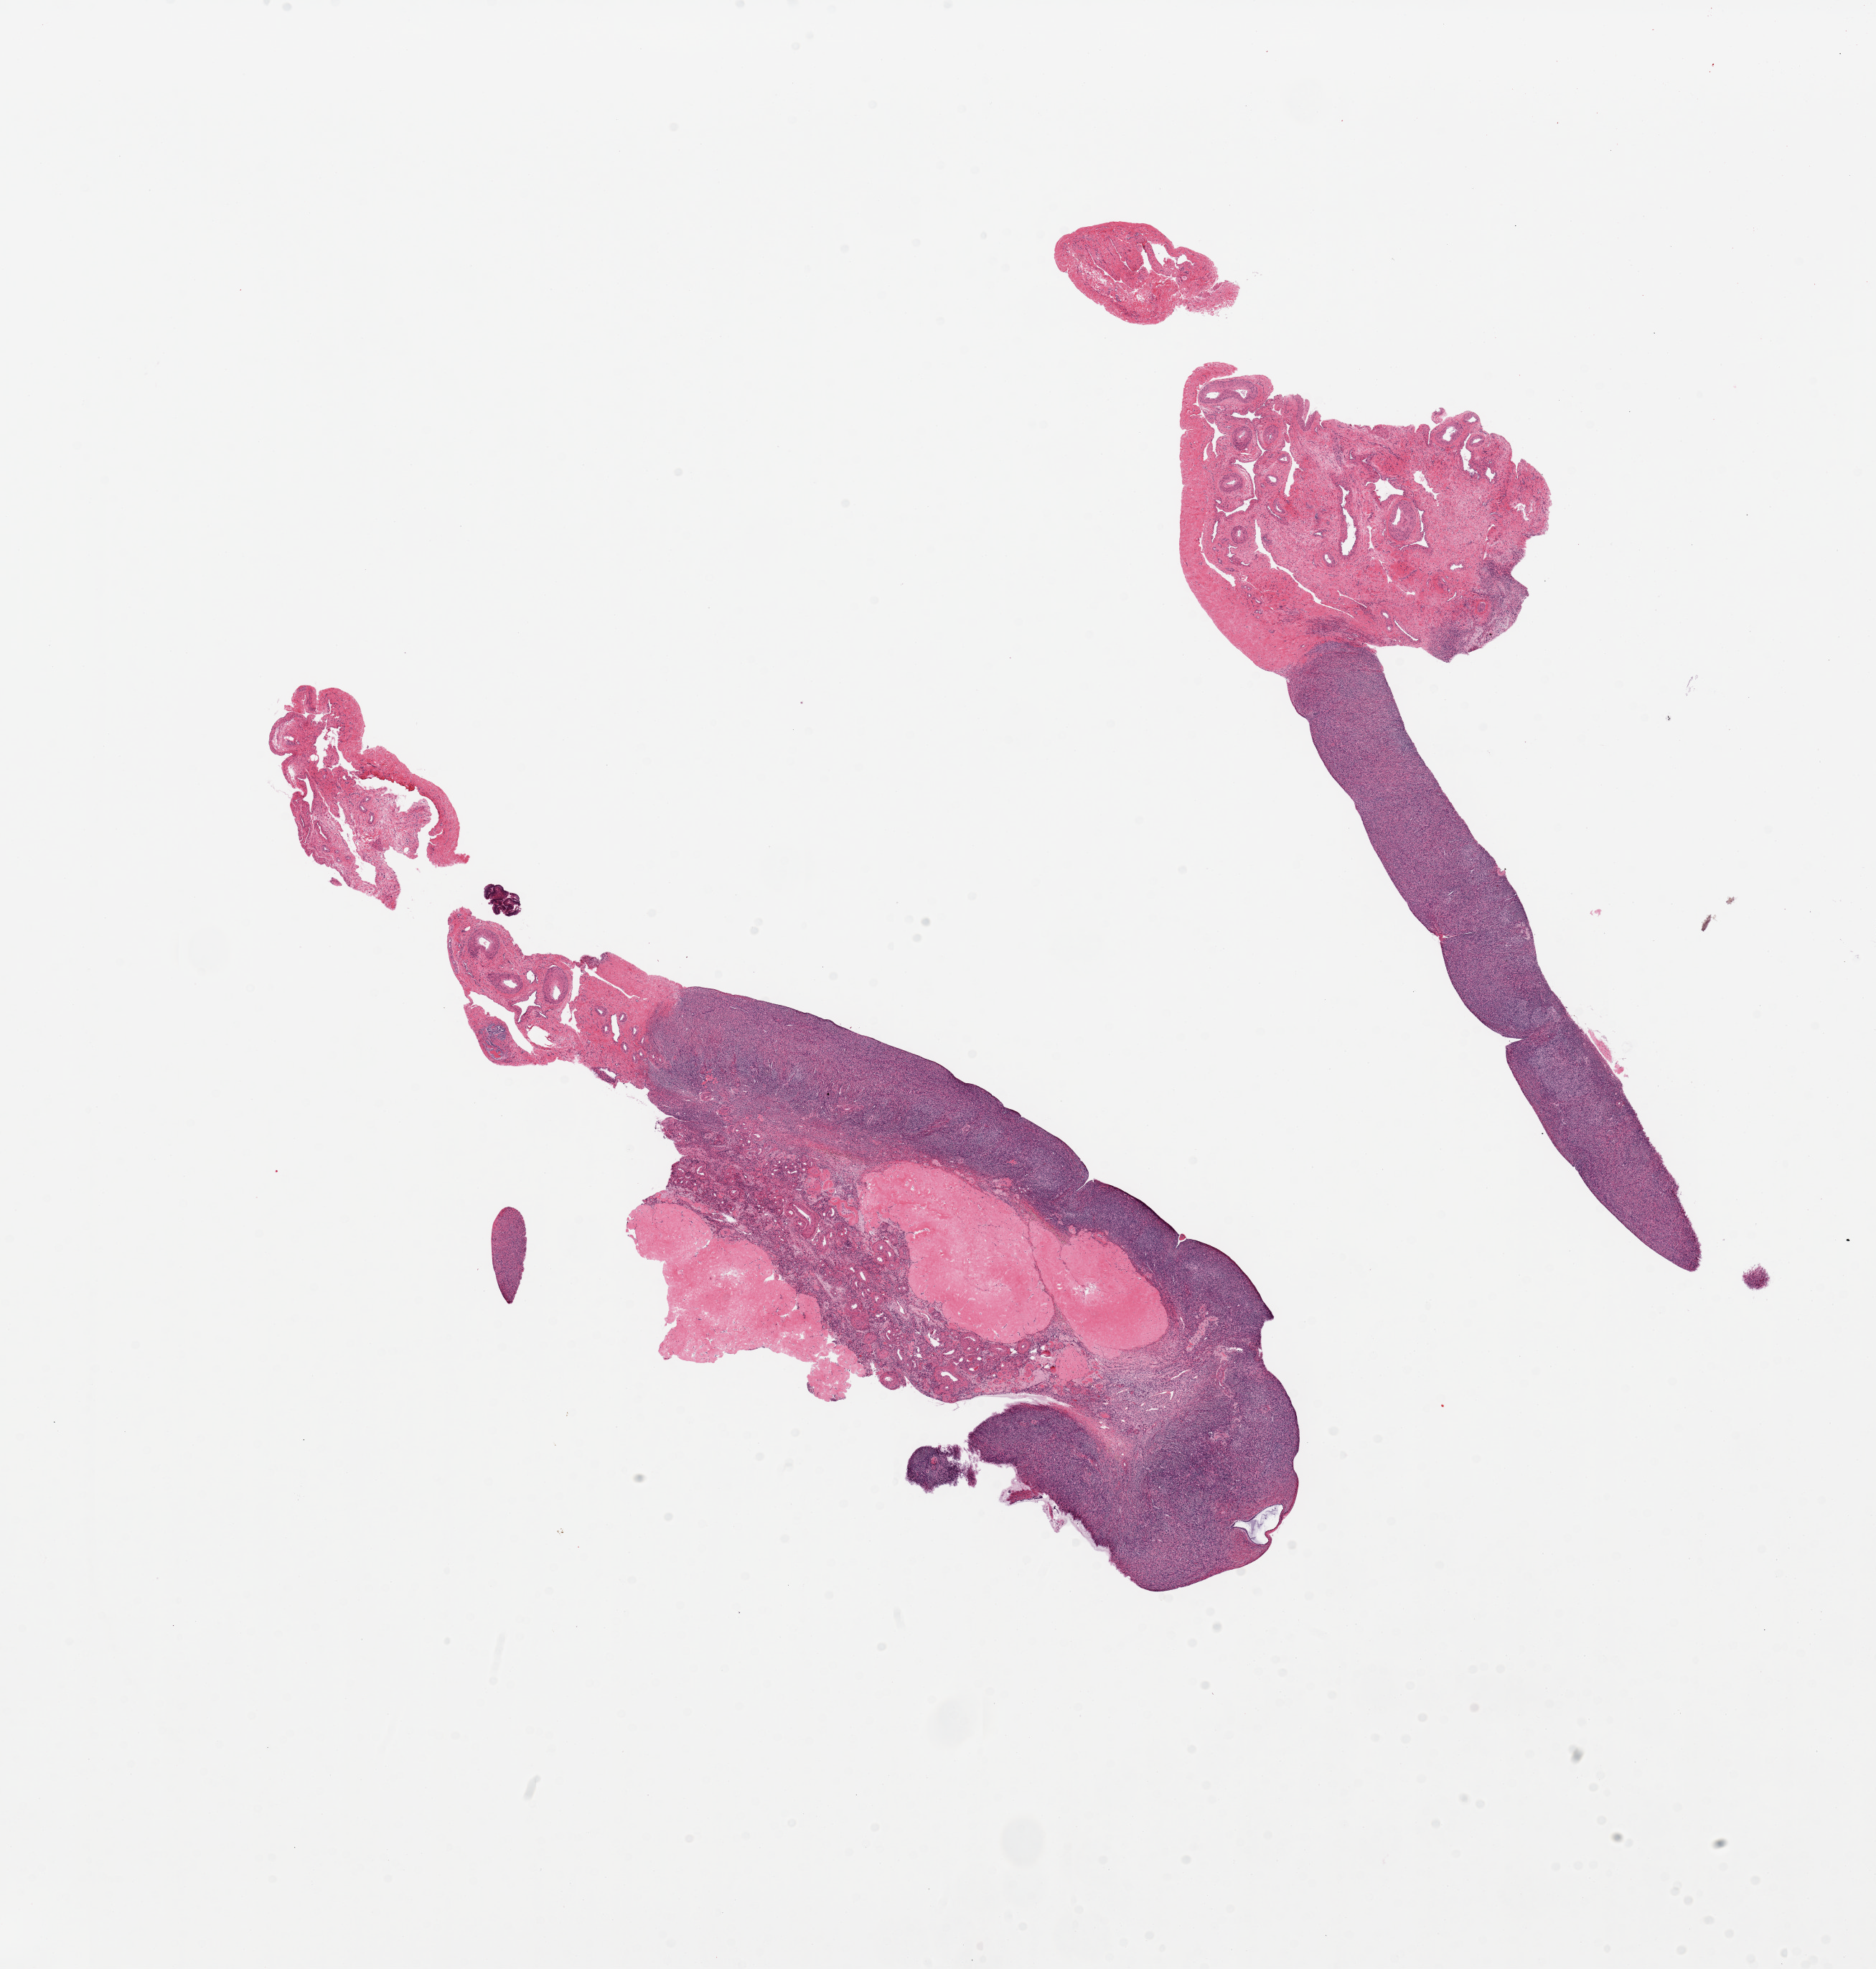
Whole-slide image, hematoxylin and eosin (H&E) stain — shown as a low-resolution overview of the whole scanned area (about 20.7 x 21.7 mm); PAXgene-fixed, paraffin-embedded tissue; section of ovary (target tissue); tissue donor sample. Donor: female.
Review note (as recorded): 2 pieces, corpora albicantia, portion of rete ovarii, floater.